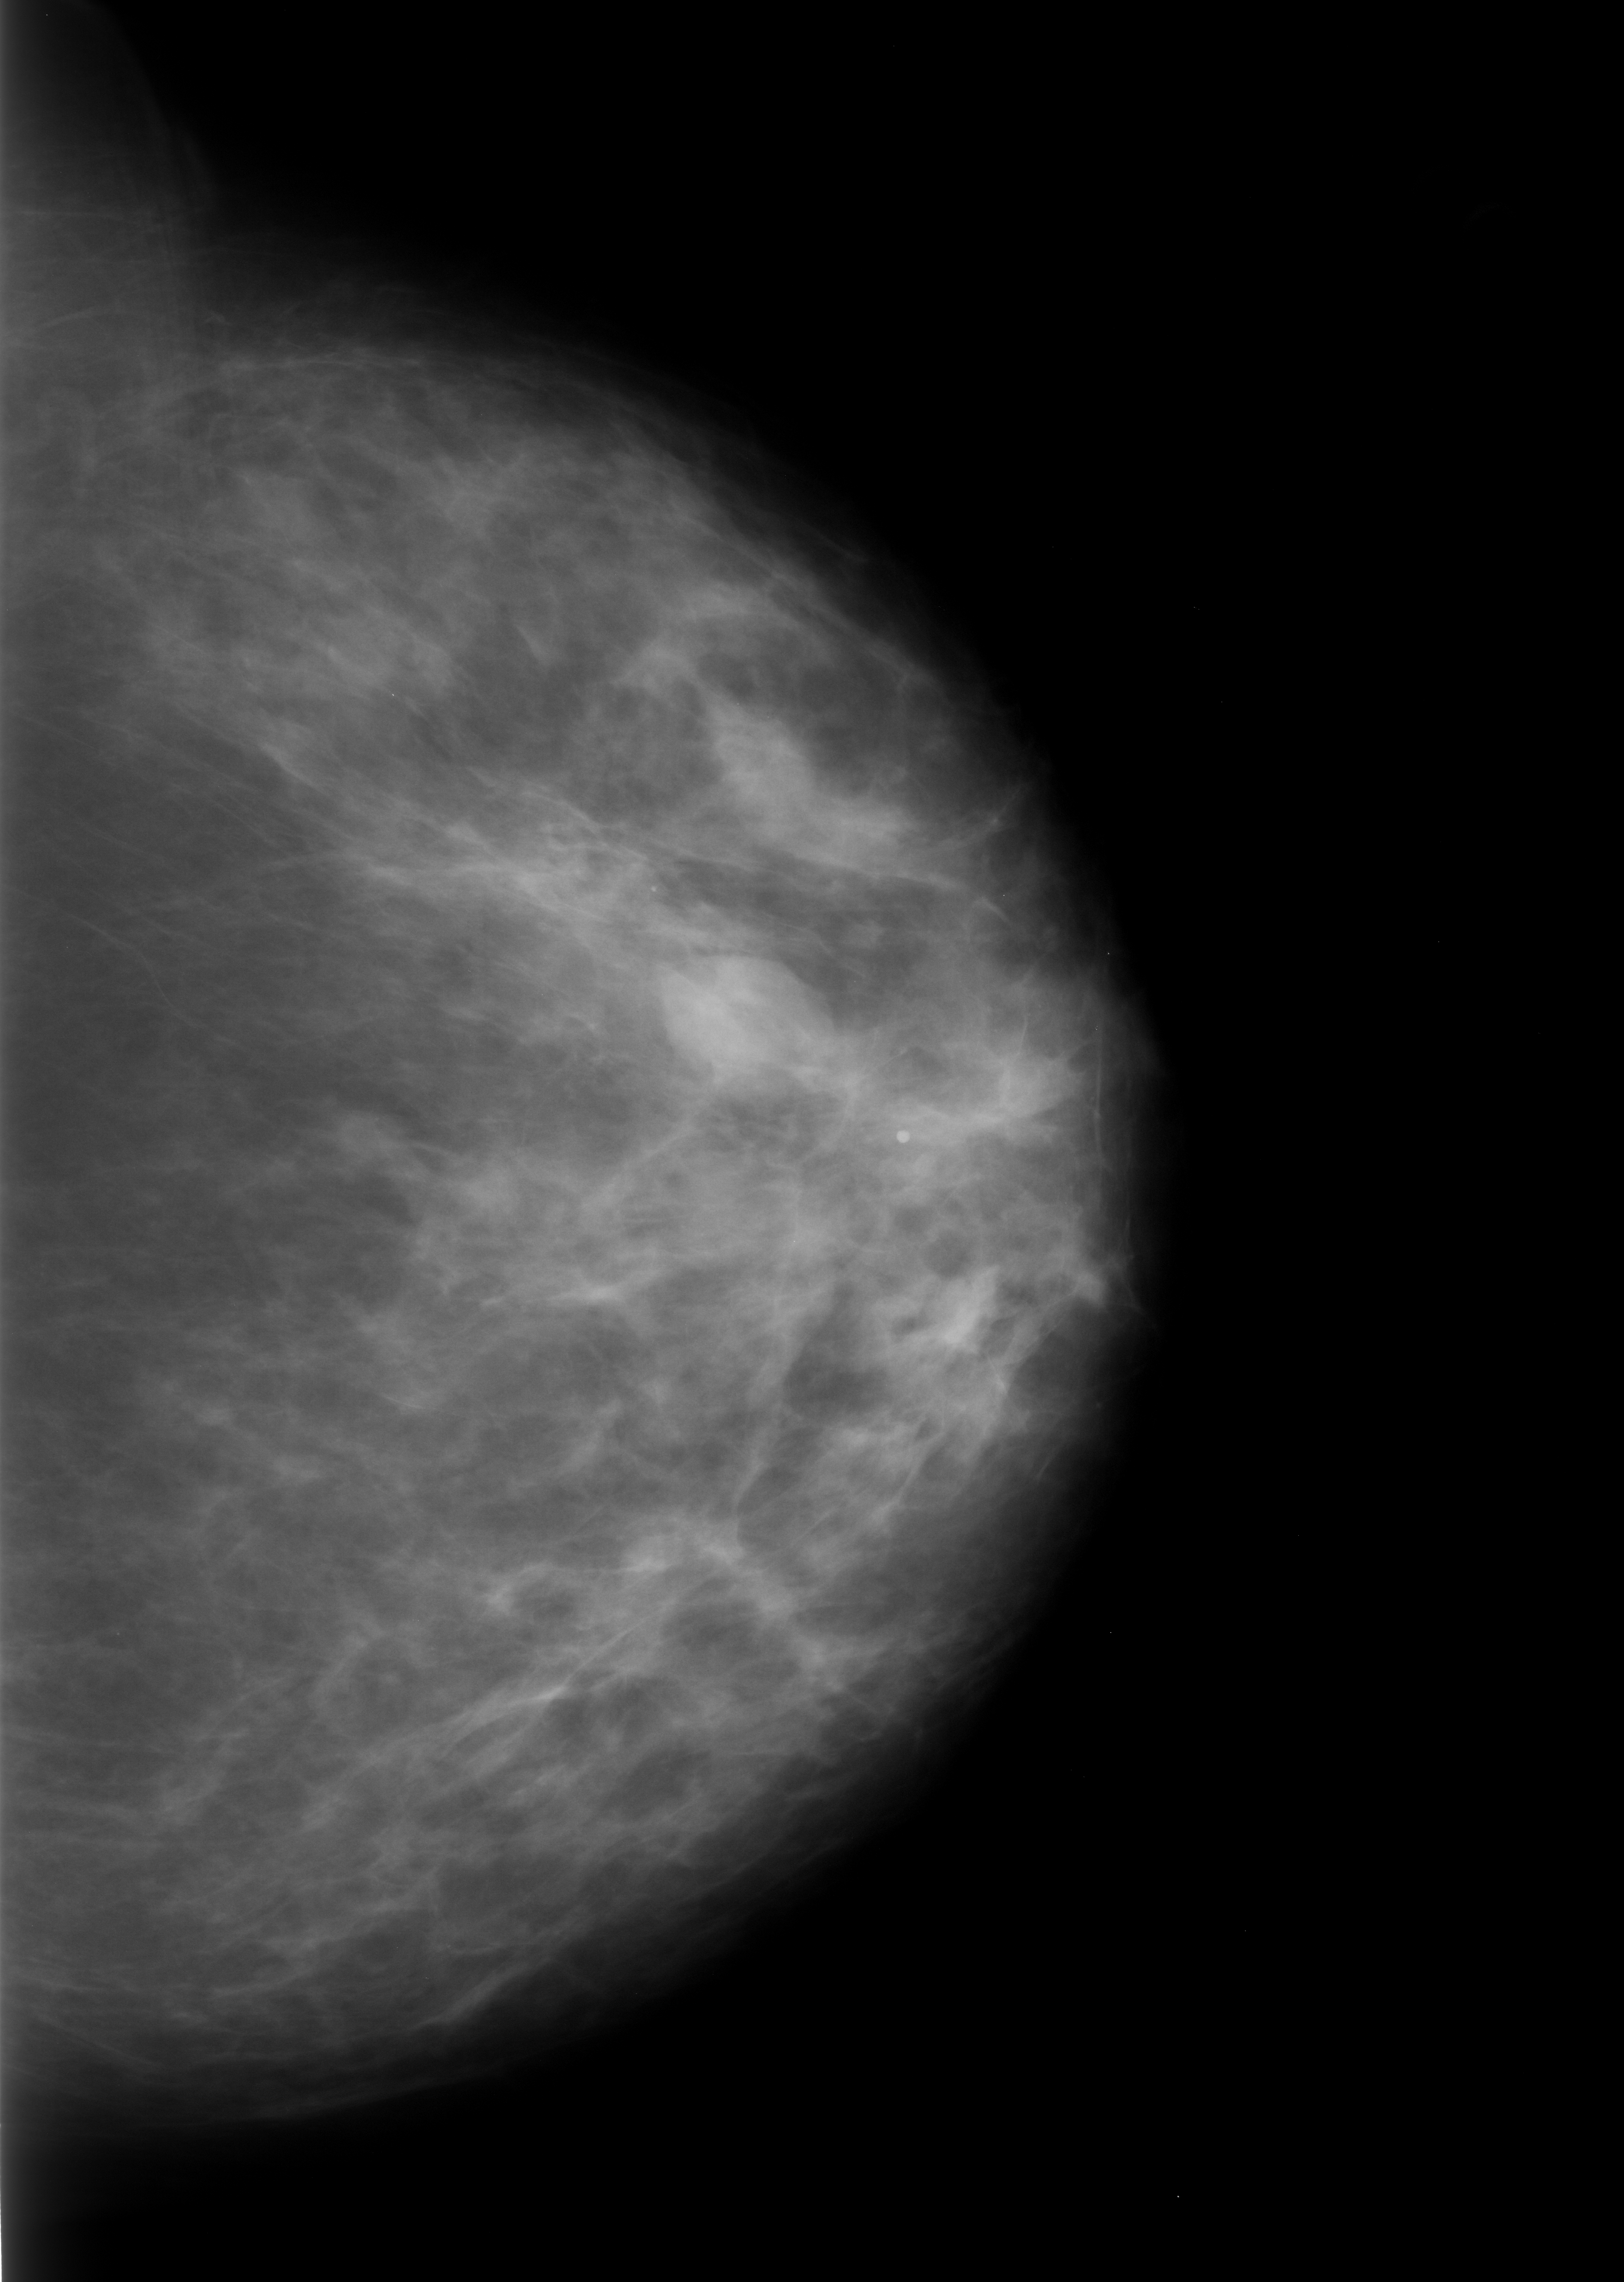
Digitized screen-film mammogram; left breast; CC view; breast composition: scattered fibroglandular densities (BI-RADS density category 2 of 4); 1624 × 2282 image matrix.
Expert-marked regions of interest on this film, with their recorded descriptors:
- mass, shape oval, margins circumscribed; BI-RADS assessment category 3; subtlety rating 5 on a 1 (subtle) to 5 (obvious) scale; pathology result (as recorded, not read from the image): benign: bounding box <659,950,814,1102> (left, top, right, bottom; pixels)